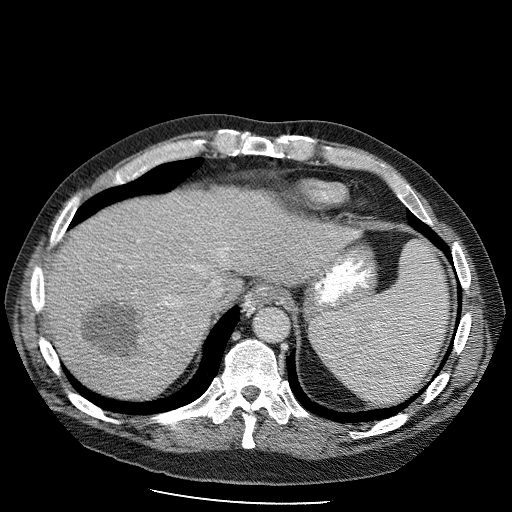
Contrast-enhanced abdominal CT (liver protocol), one axial slice; position 84 of 98 along the scan axis; reconstruction kernel STANDARD; 120 kVp; soft-tissue window (W 400 / L 40 HU); 512 × 512 image matrix, field of view 400 × 400 mm. Case-level facts recorded for this patient, not image findings: diagnosis: hepatocellular carcinoma (patient treated with transarterial chemoembolisation; whether this scan precedes or follows treatment is not stated here); TNM stage (as recorded): Stage-II; Child-Pugh class: B.
Annotated regions visible in this slice (semi-automatically segmented with operator editing):
- liver parenchyma outside the tumour (the mass and vessels are separate outlines, so this box may not span the whole liver): box from (x=40, y=190) to (x=356, y=392) px
- mass: (x=76, y=292)–(x=151, y=361)